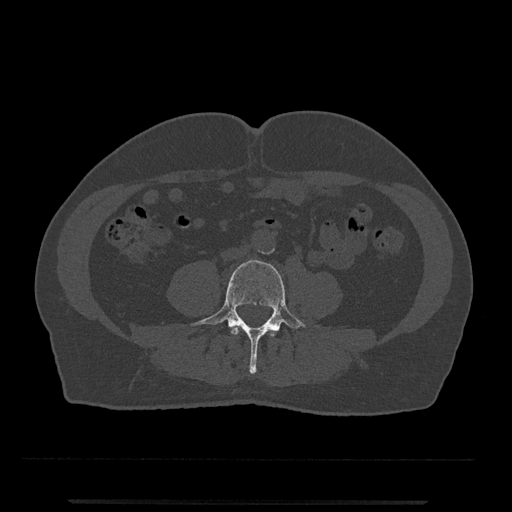
CT including the spine, one axial slice; position 143 of 797 along the scan axis; bone window (W 1800 / L 400 HU); 0.5 mm slice thickness; 512 × 512 image matrix, field of view 419 × 419 mm. Patient: male, 63 years. Case-level facts recorded for this patient, not image findings: primary cancer: prostate.
Annotated regions visible in this slice (semi-automatically segmented with operator editing):
- L3 vertebra: bounding box [x1, y1, x2, y2] px = [231, 326, 276, 337]
- L4 vertebra: [191, 260, 306, 374]